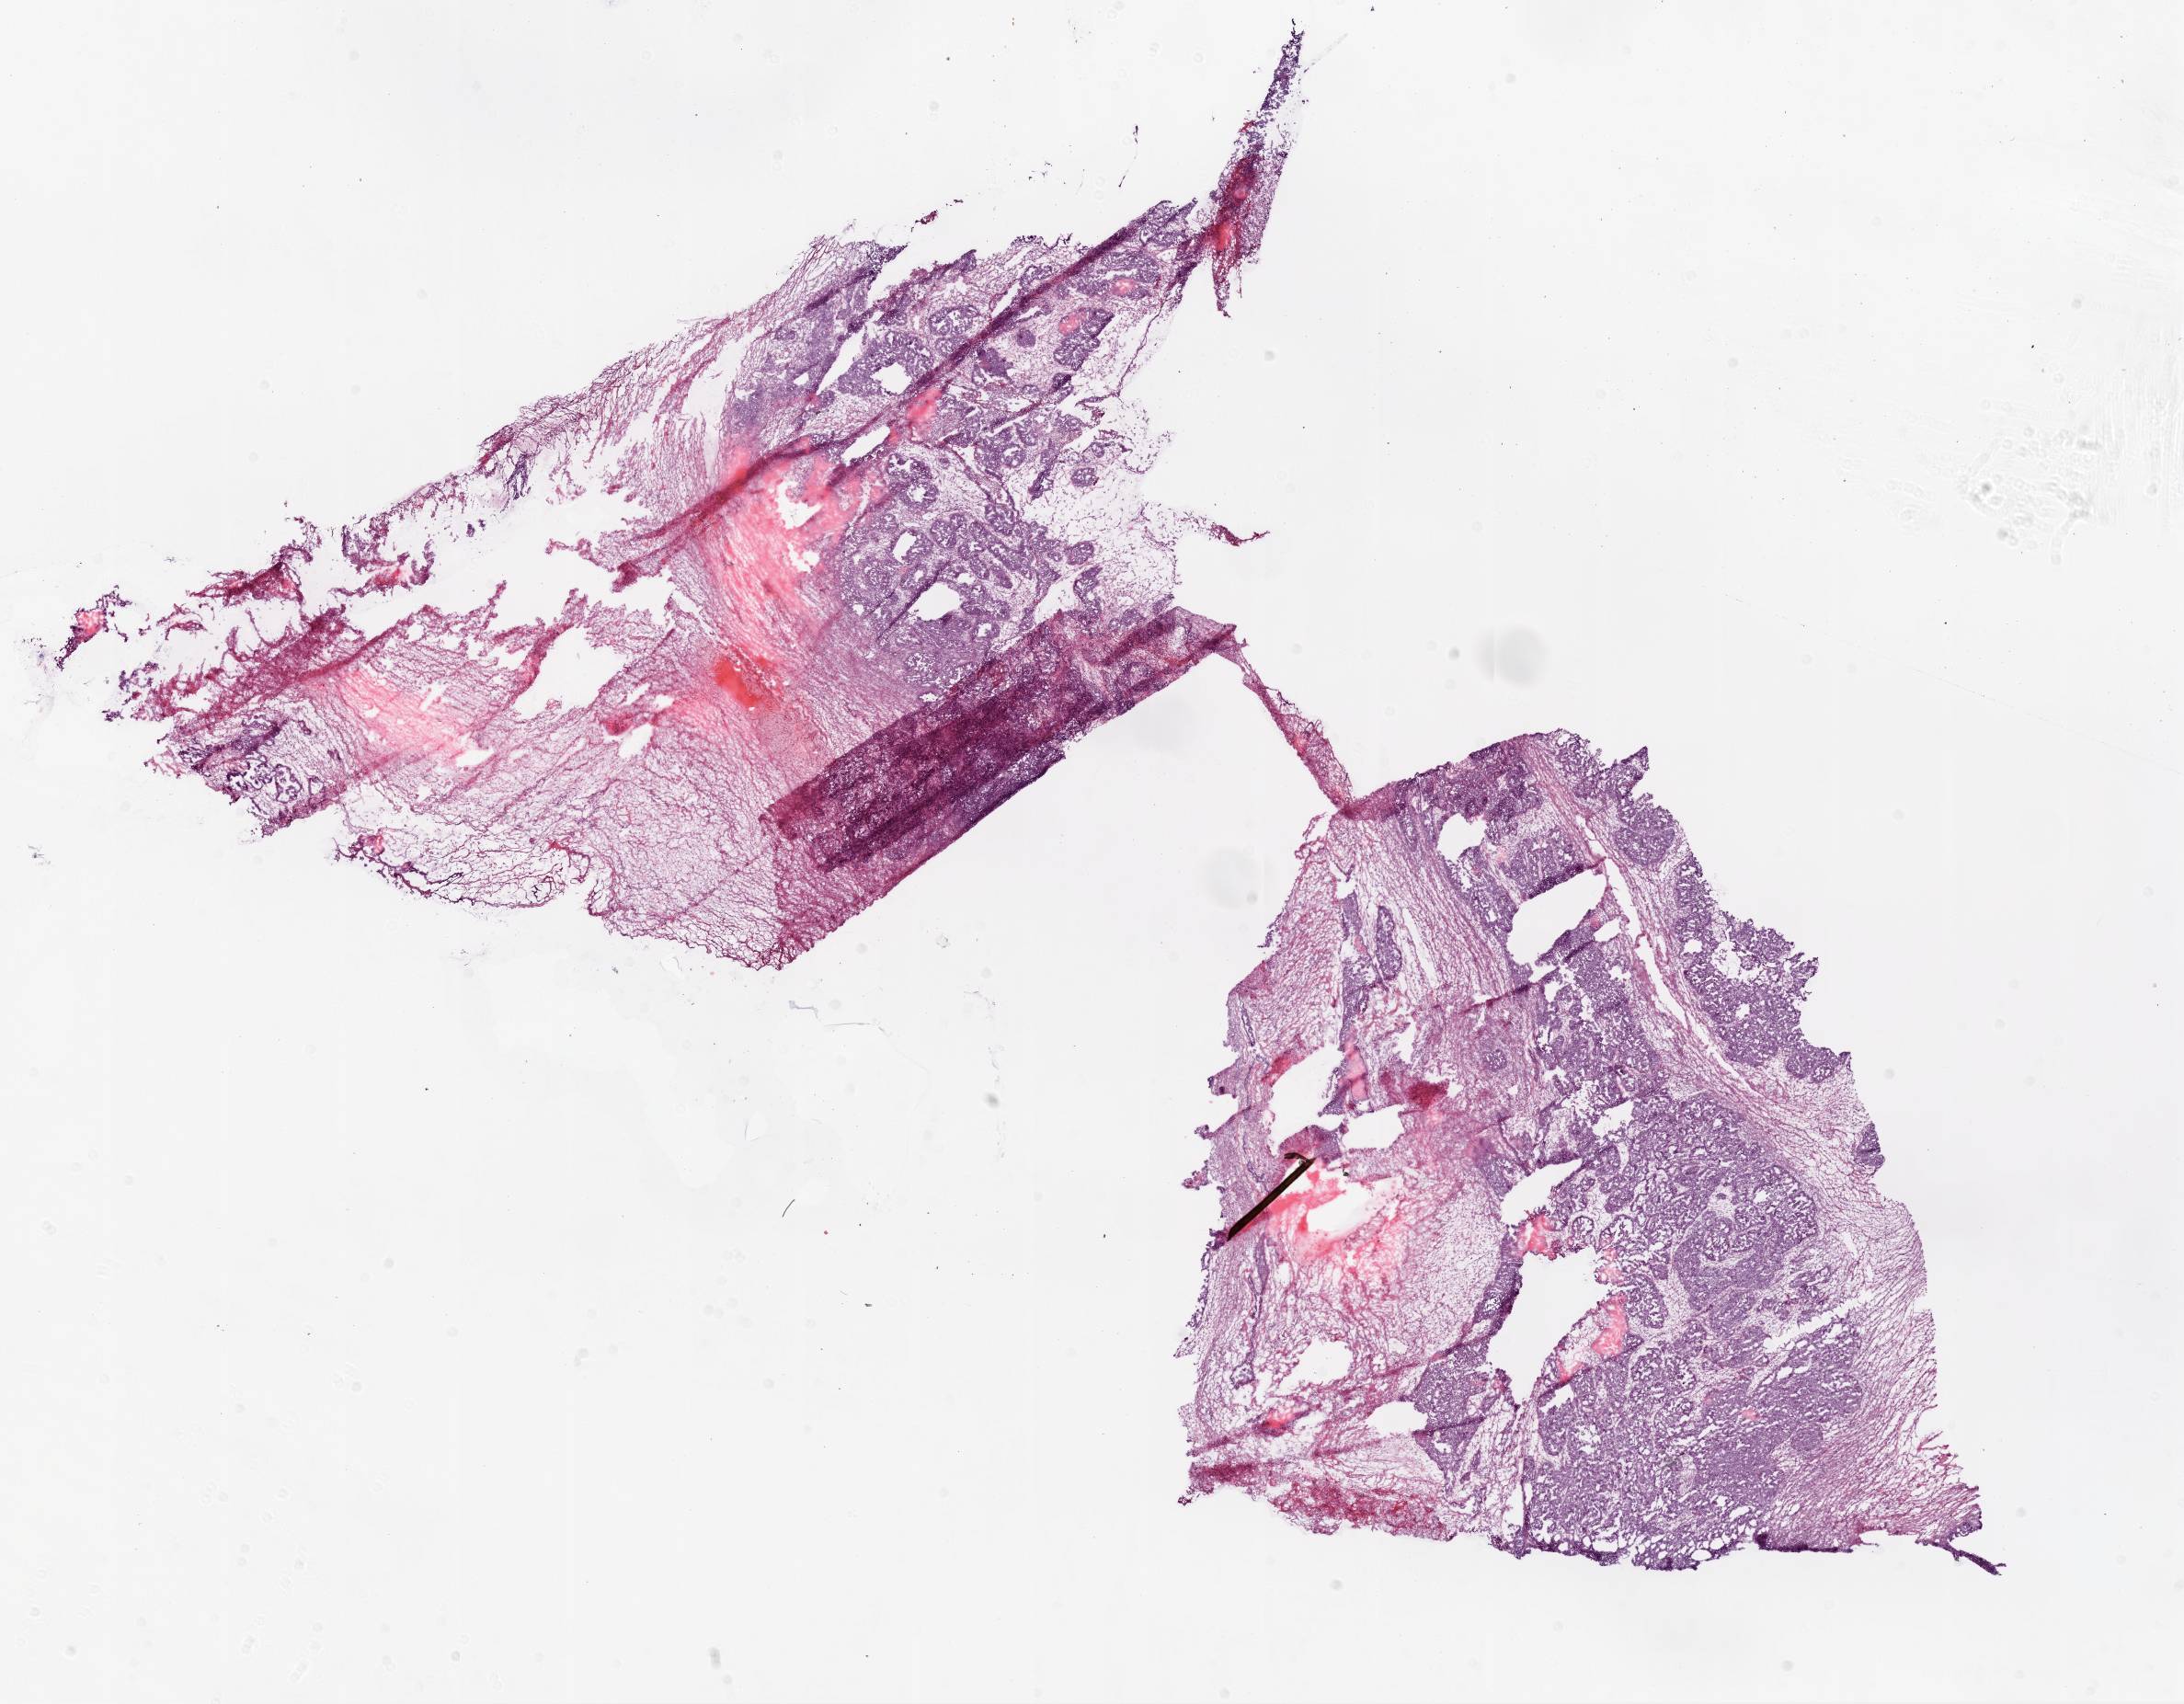
Digitized H&E tissue section (whole slide) — low-resolution overview of the scanned area, about 19.1 x 14.9 mm. Frozen section from the bottom of the tissue portion. Sample: primary tumour, ovary. Female, age 71 years at initial diagnosis. Histologic grade: G2 (moderately differentiated). Composition of this section per pathologist review: tumour cells 80%, tumour nuclei 80%, normal cells 0%, stromal cells 20%, necrosis 0%. Infiltration values recorded for this section: lymphocyte infiltration 0%, monocyte infiltration 0%, neutrophil infiltration 0%.
Pathologic diagnosis: Serous cystadenocarcinoma, NOS. FIGO stage: IIC. Laterality: bilateral.